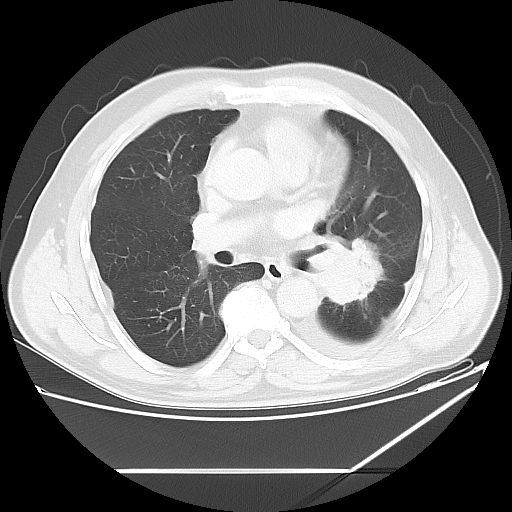
Chest CT, one axial slice. Position 32 of 60 along the scan axis. Reconstruction kernel LUNG. Lung window (W 1500 / L -600 HU). 5 mm slice thickness. 512 × 512 image matrix, field of view 395 × 395 mm. Patient: male, 62 years. From the clinical record (not read from this slice): clinical TNM (as recorded): T3 N0 M1.
Annotated regions visible in this slice (bounding box drawn by a radiologist):
- lung tumour (recorded histology: adenocarcinoma): bounding box (x1, y1, x2, y2) in pixels: (317, 236, 390, 311)
- lung tumour (recorded histology: adenocarcinoma): (322, 232, 387, 311)